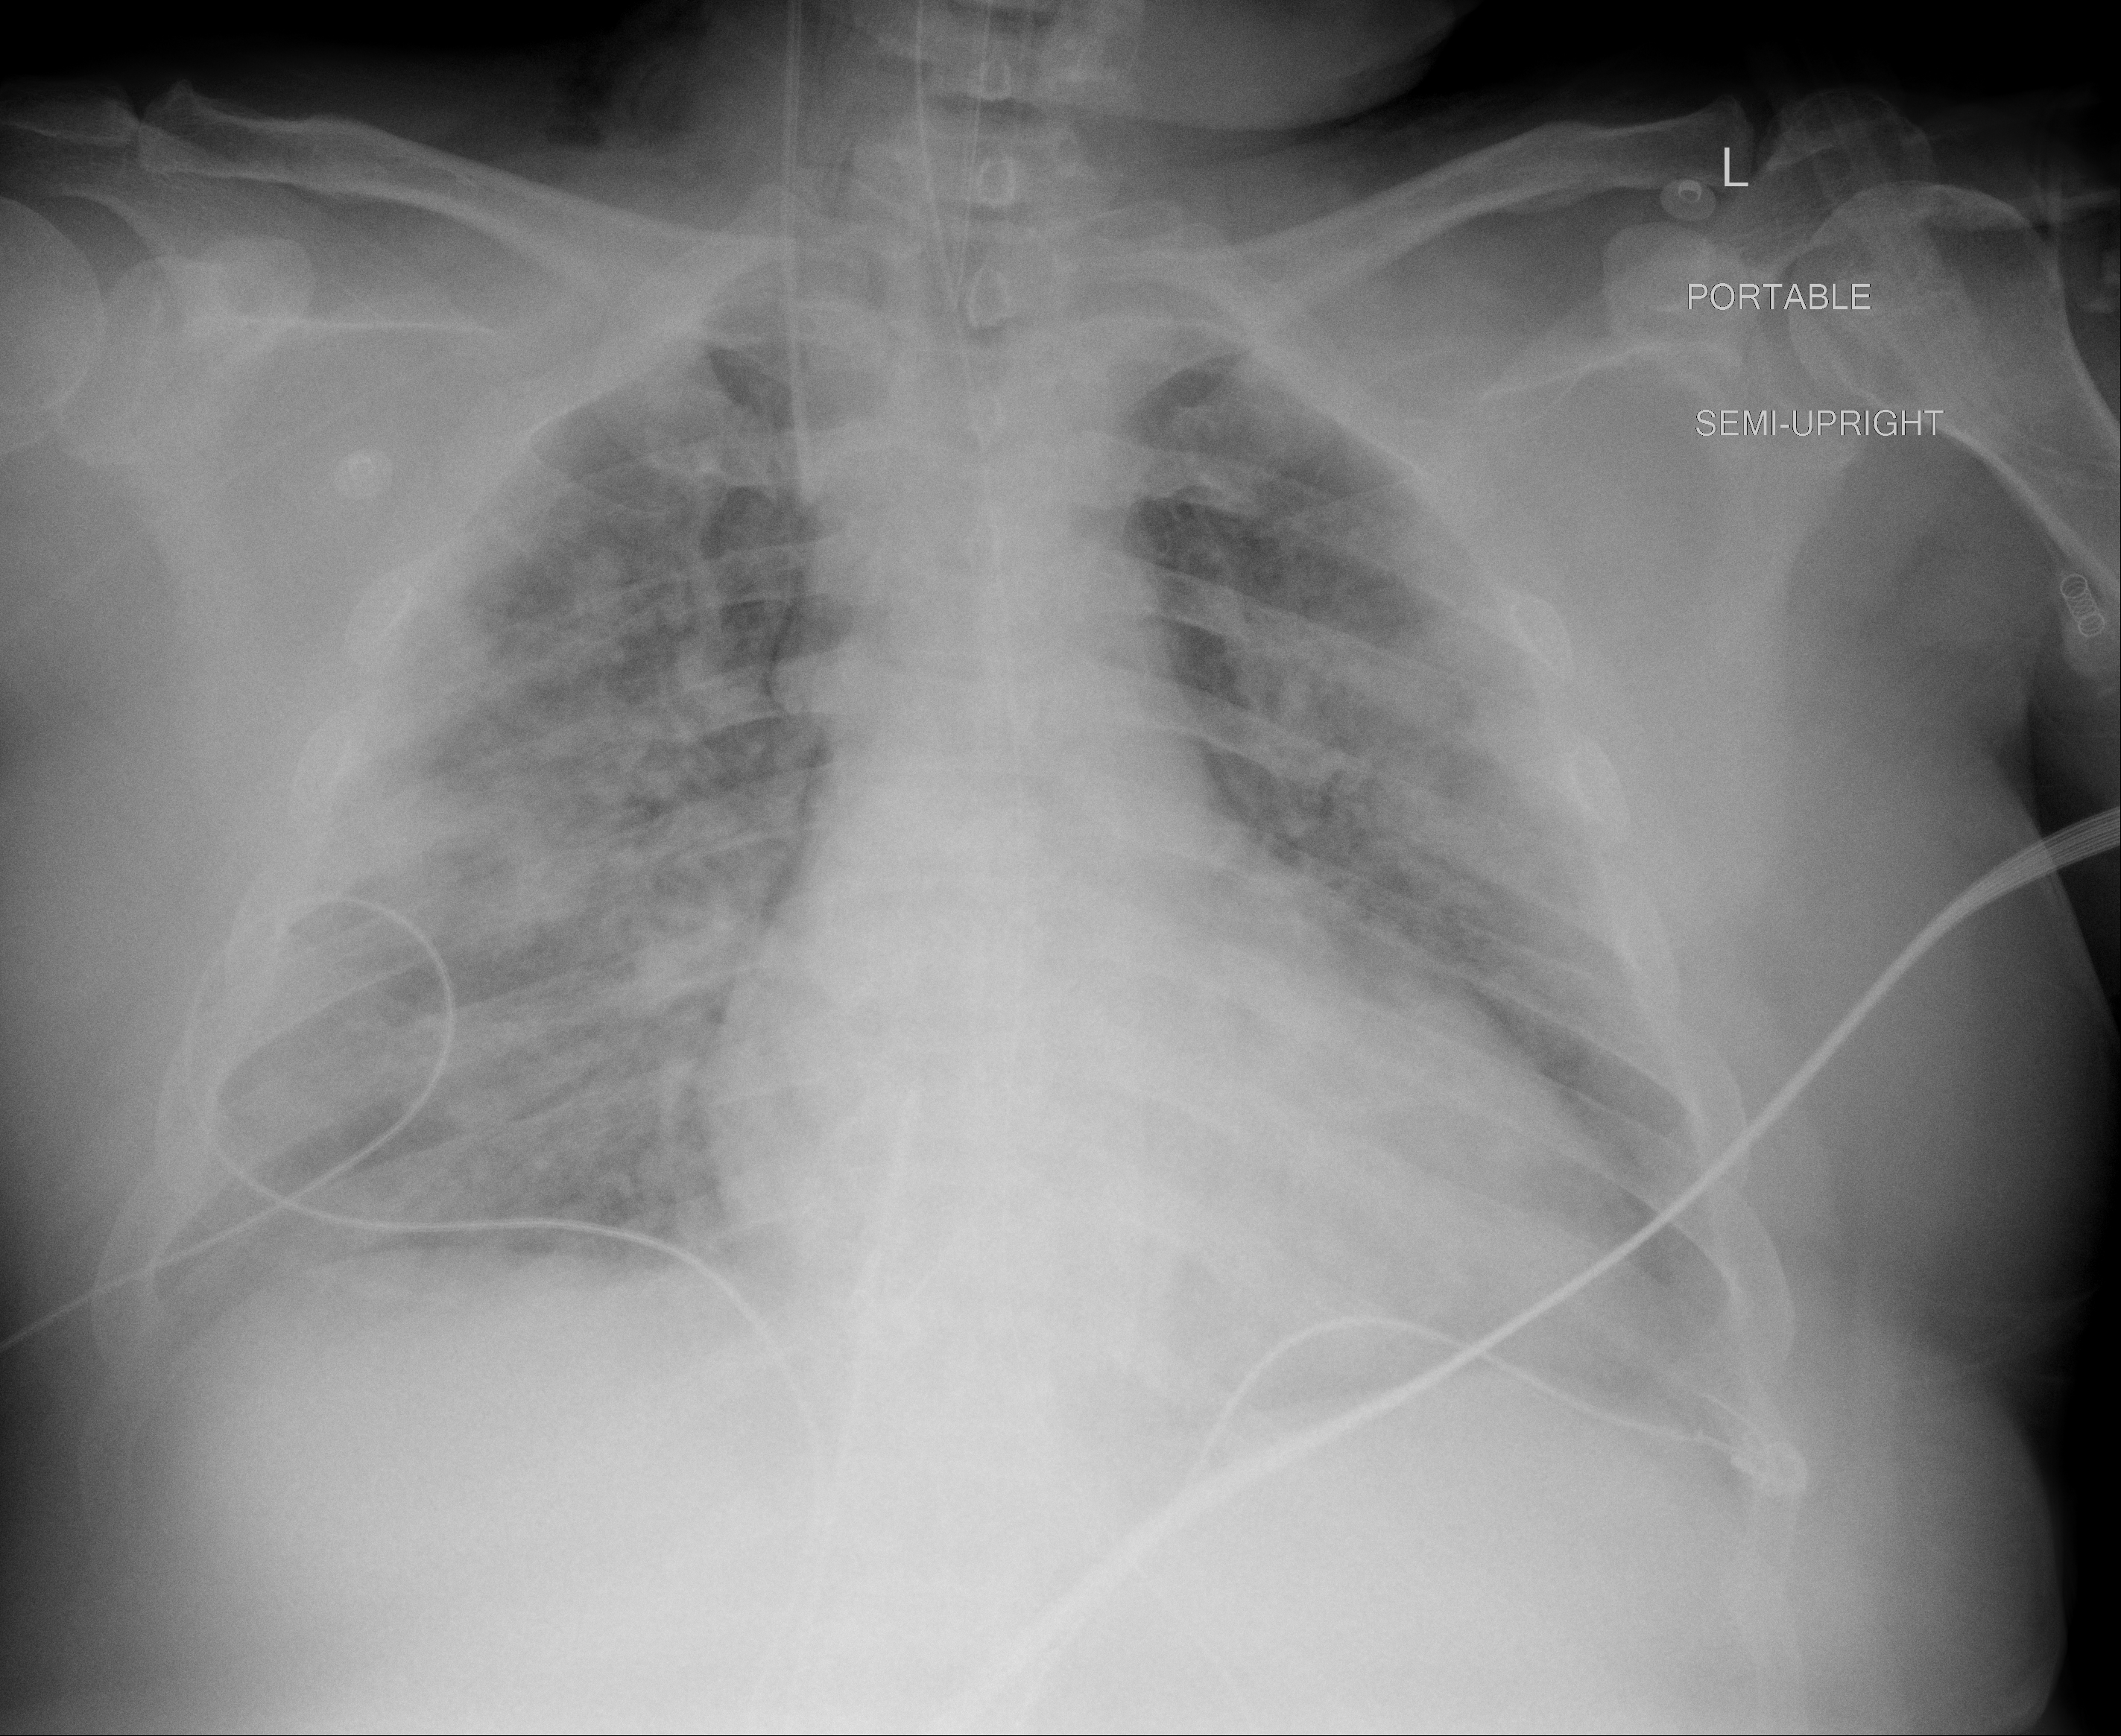
Chest X-ray (portable), AP projection. Male patient, age 55 years; imaged 5 days after the COVID-19 diagnosis.
Radiologist's key findings for this exam: Fairly diffuse airspace disease throughout the lungs shows no improvement.